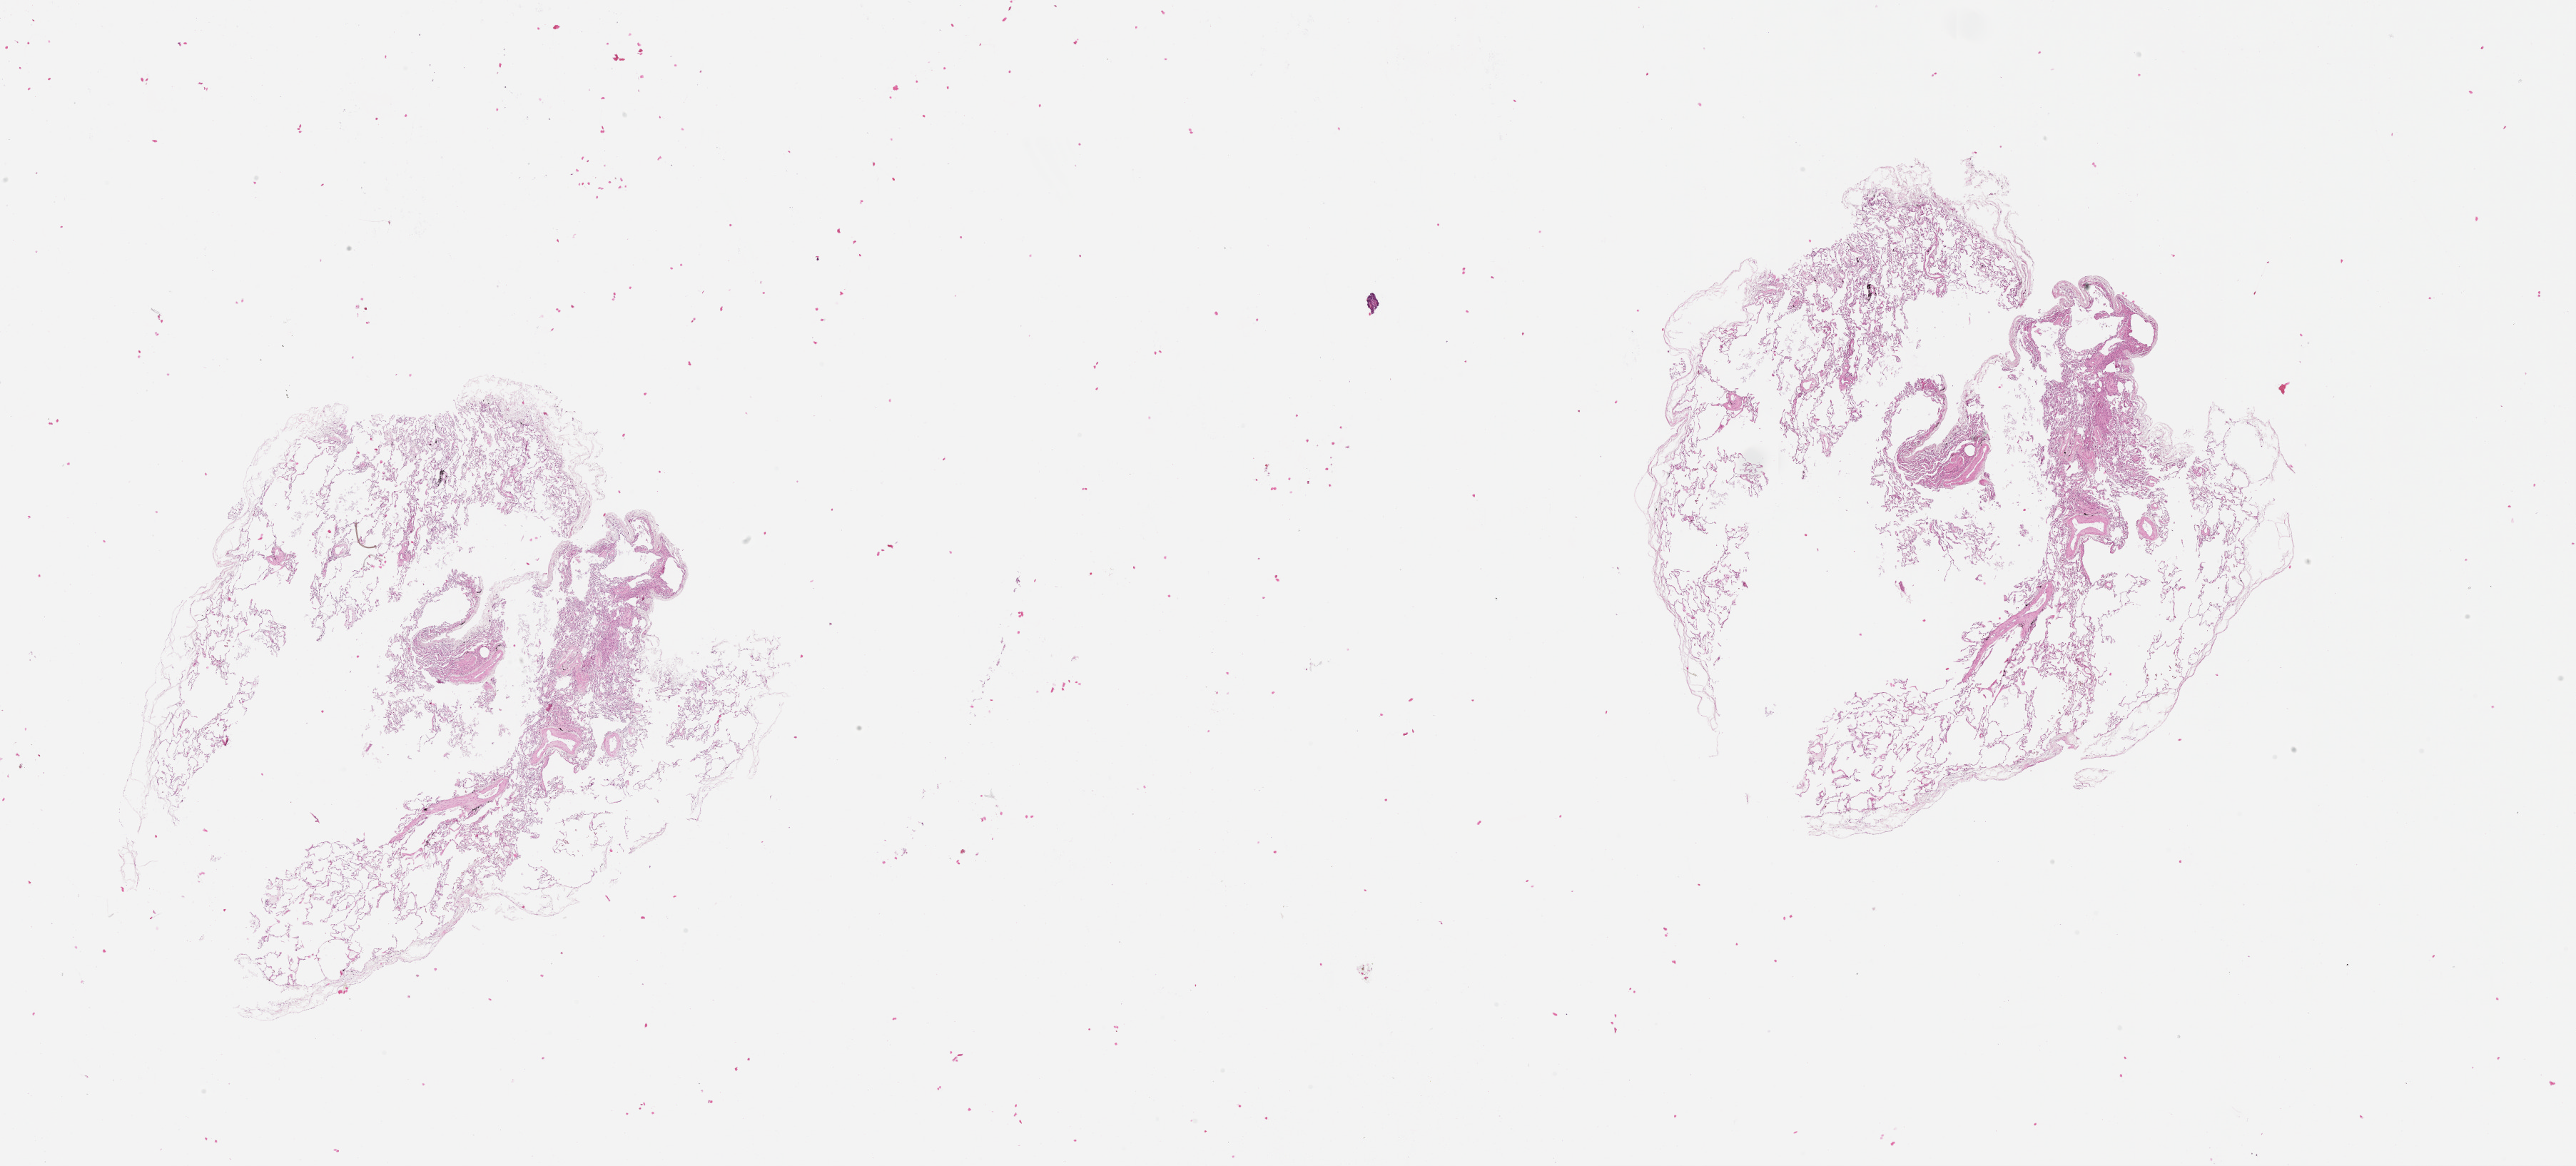
H&E-stained whole-slide image — shown as a low-resolution overview of the whole scanned area (about 29.1 x 13.2 mm, slide scanned at 20x); lung, tissue type not recorded.
Patient diagnosis (cohort enrolment): lung adenocarcinoma (lung).